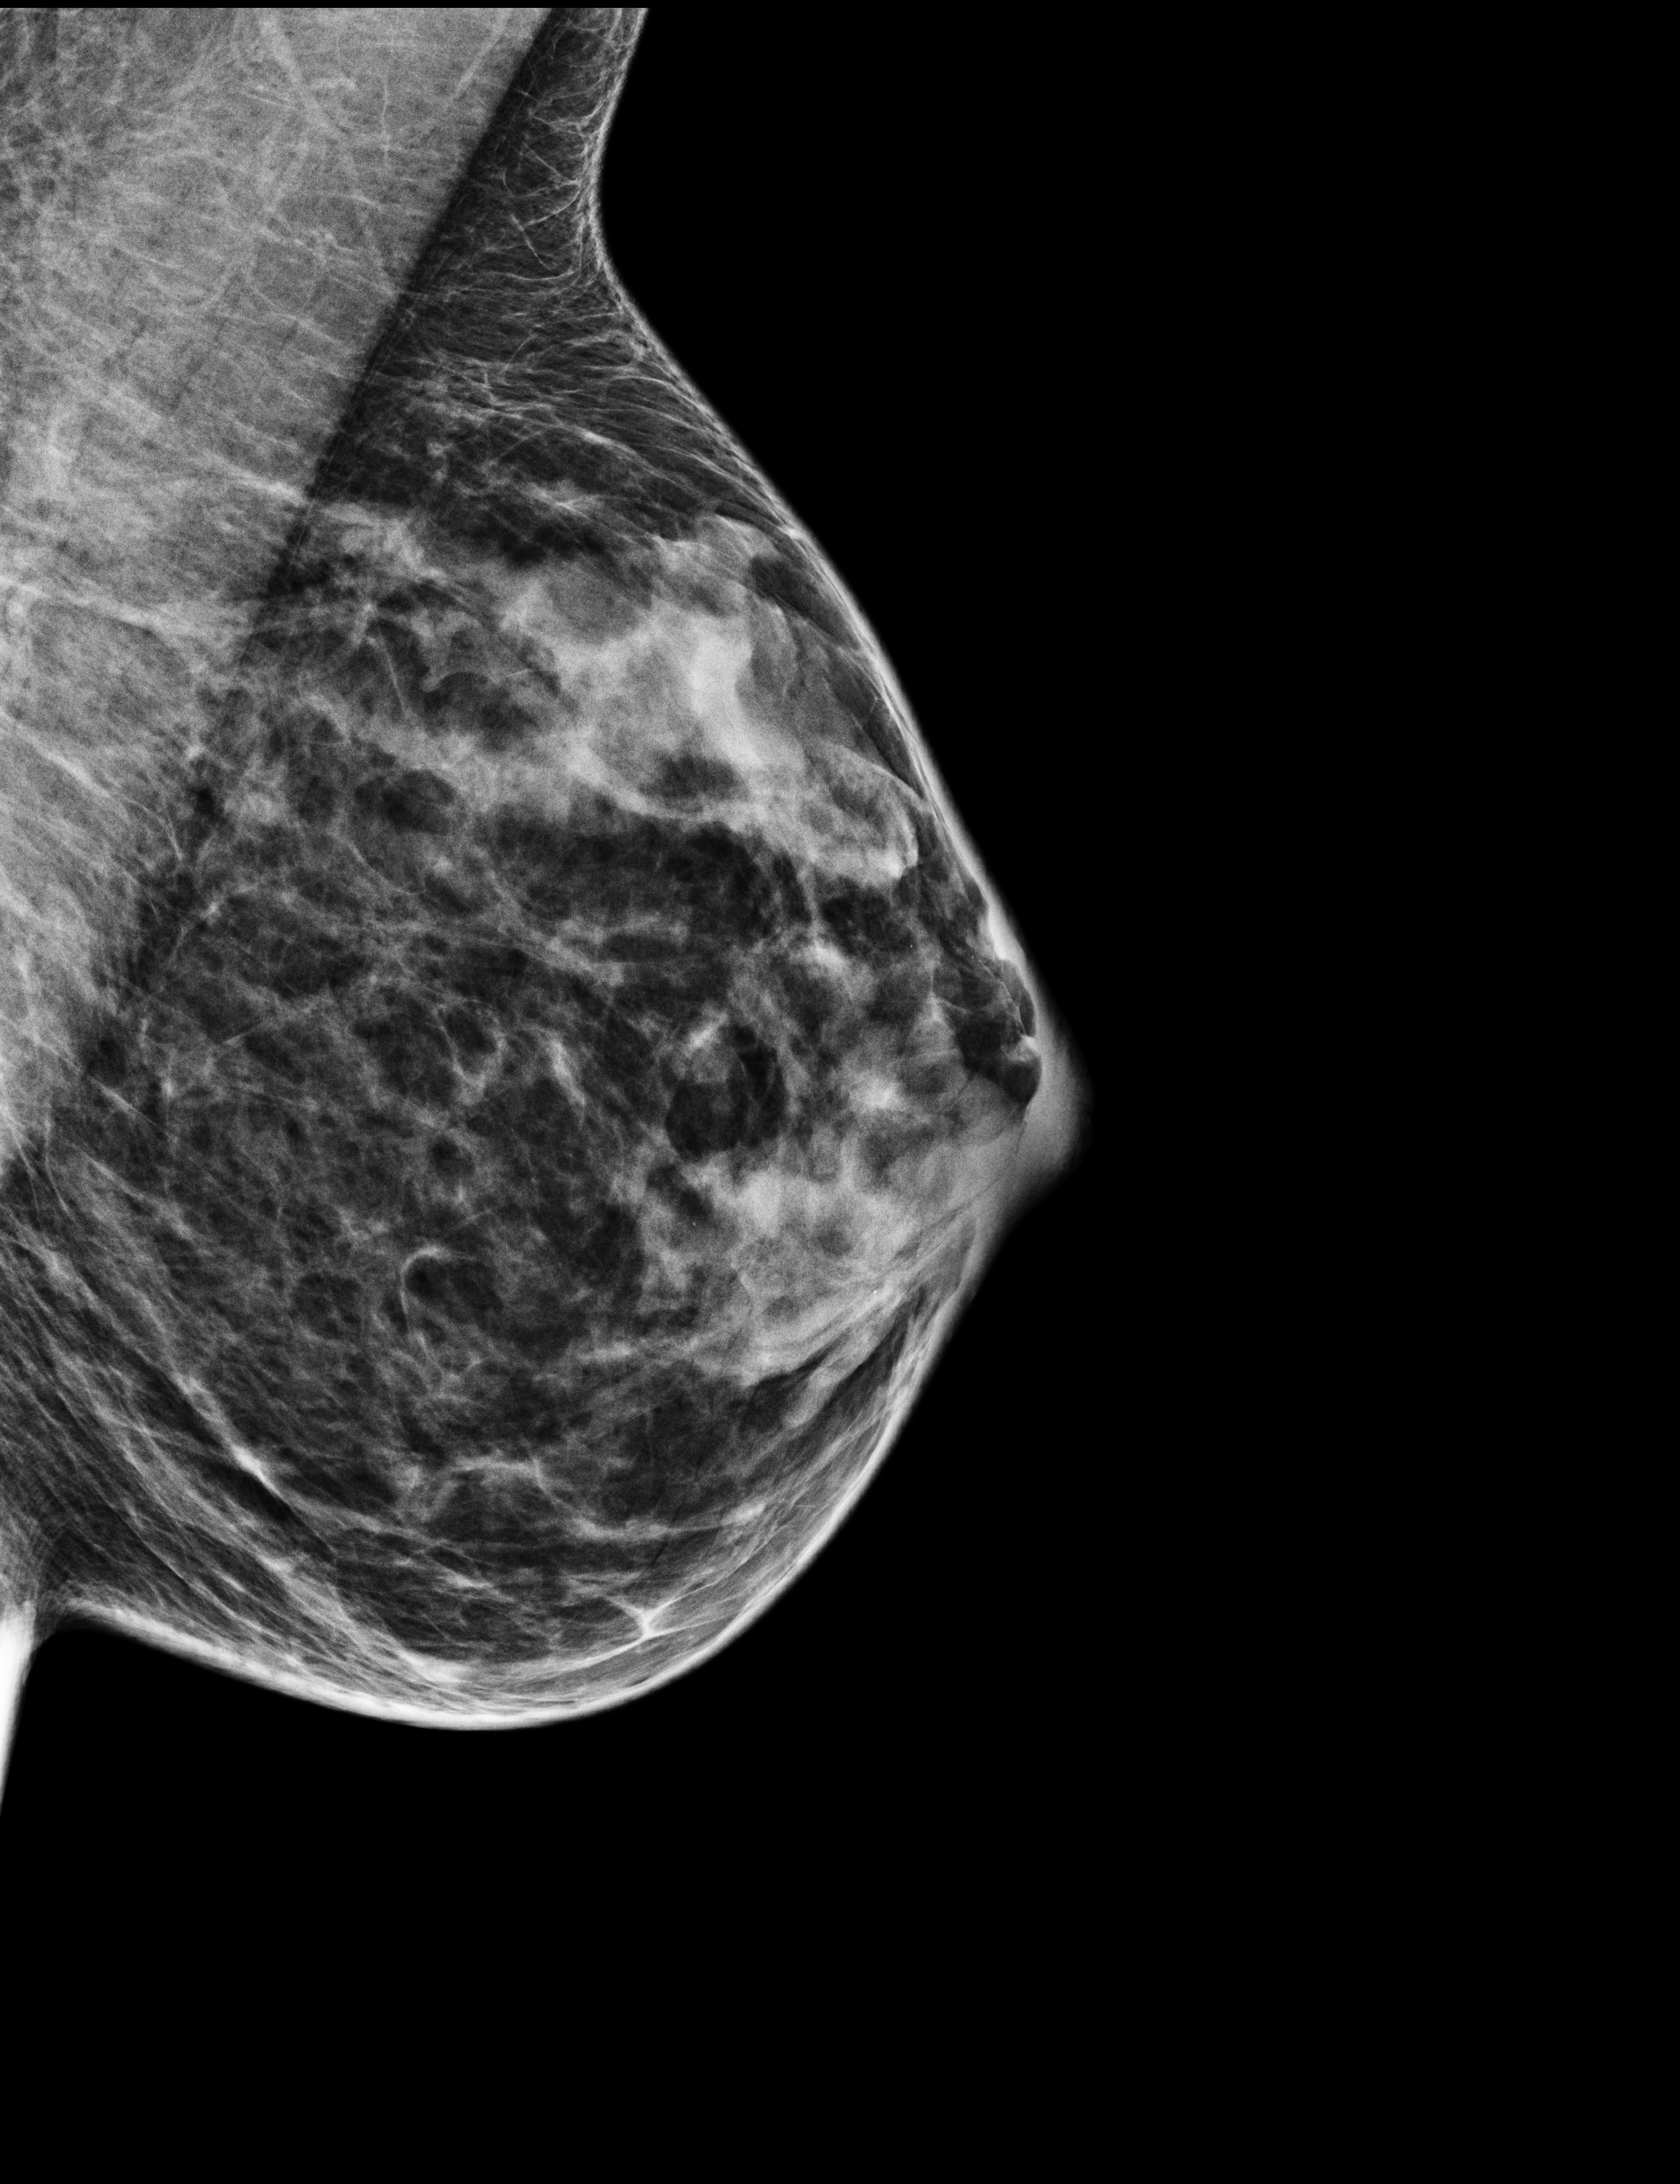
Digital mammogram (FFDM); left breast; medio-lateral oblique projection; annual screening mammography examination. Patient aged 44 years (female).
BI-RADS breast density category at the screening exam (both breasts, scale 1–4): 3. Final BI-RADS assessment for this screening round (tomosynthesis exam, both breasts): category 2. Recall: recalled for additional imaging after this screen.